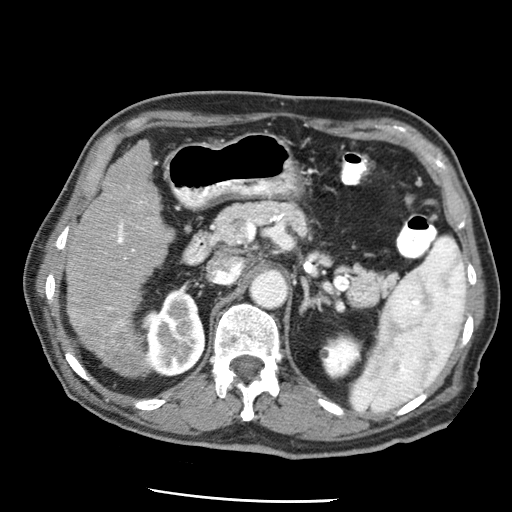
Contrast-enhanced abdominal CT (liver protocol), one axial slice. Position 23 of 79 along the scan axis. Reconstruction kernel STANDARD. Soft-tissue window (W 400 / L 40 HU). 512 × 512 image matrix. Case-level facts recorded for this patient, not image findings: diagnosis: hepatocellular carcinoma (patient treated with transarterial chemoembolisation; whether this scan precedes or follows treatment is not stated here); TNM stage (as recorded): Stage-IIIA; Child-Pugh class: A; tumour nodularity: multinodular; tumour size: 7 cm.
Outlined on this slice (semi-automatic segmentation, software-assisted and operator-edited):
- liver parenchyma outside the tumour (the mass and vessels are separate outlines, so this box may not span the whole liver): bounding box [x1, y1, x2, y2] px = [66, 140, 172, 370]
- liver vessels: [73, 201, 144, 342]